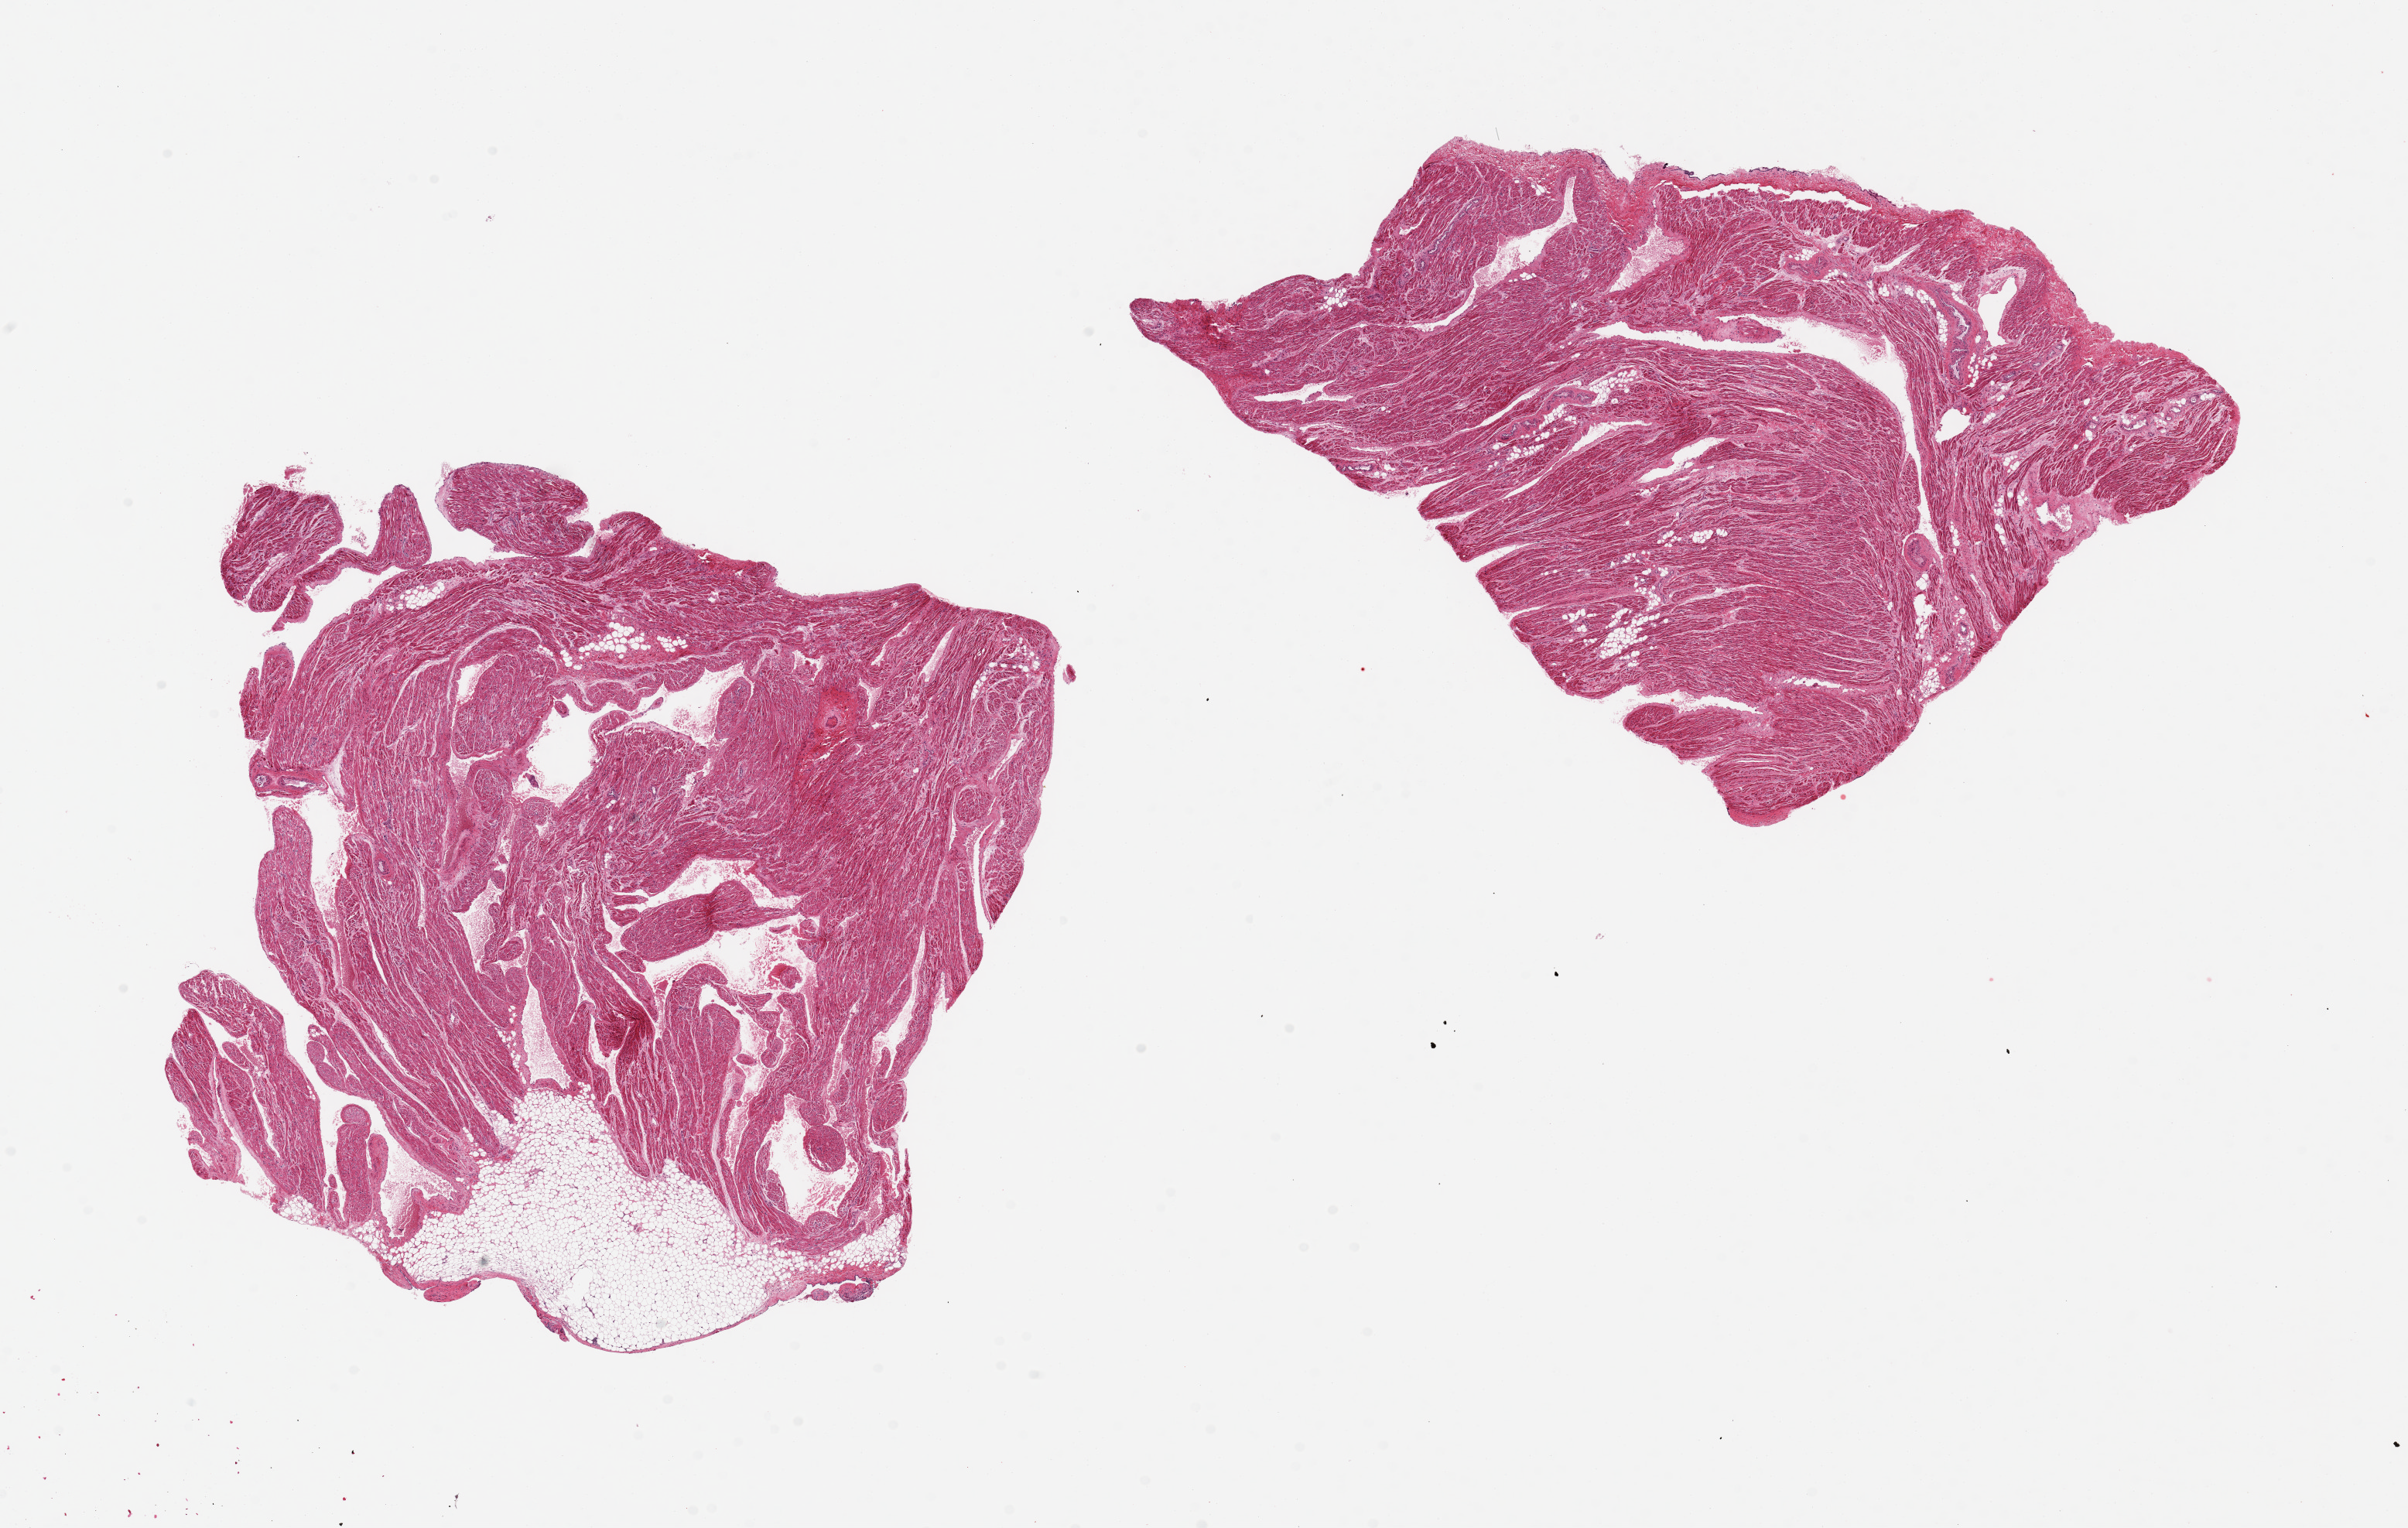
Whole-slide image, haematoxylin and eosin stain — shown as a low-resolution overview of the whole scanned area (about 24.6 x 15.6 mm); PAXgene-fixed, paraffin-embedded tissue; target tissue: auricular appendage; tissue donor sample. Male donor.
Pathologist's review note for this sample: 2 pieces ~9x9mm.